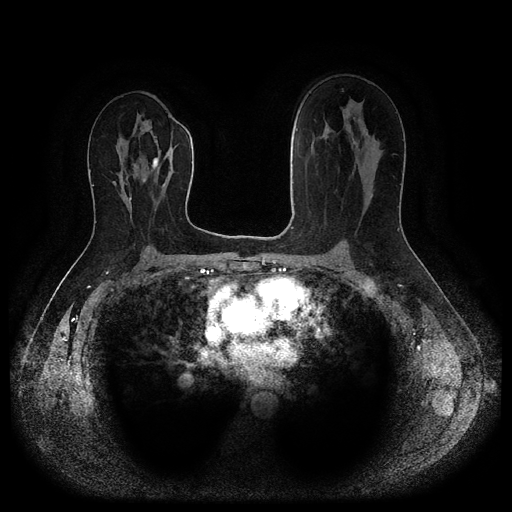
Breast MRI (dynamic contrast-enhanced, multi-phase), one axial slice; position 57 of 116 along the scan axis; dynamic contrast-enhanced series, time point 2 of 5 at this slice position (early post-contrast); 1.5 T; TE 2.6 ms, TR 5.3 ms; 2.2 mm slice thickness; 512 × 512 image matrix, field of view 360 × 360 mm. Female patient, age 53 years.
Annotated regions visible in this slice (semi-automatic segmentation, software-assisted and operator-edited):
- breast lesion (labelled benign in the annotation): bounding box (x1, y1, x2, y2) in pixels: (151, 157, 159, 168)